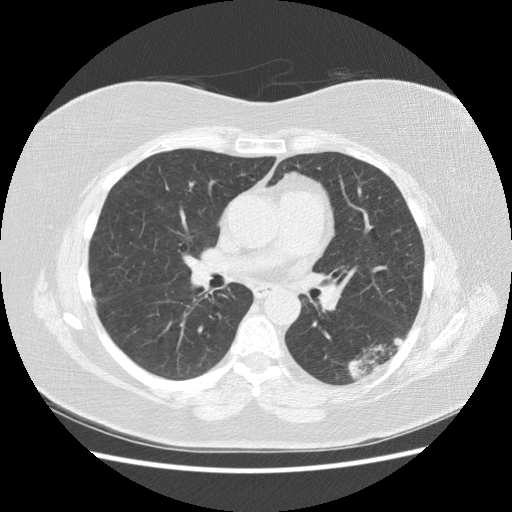
Low-dose screening chest CT, one axial slice. Slice 84 of 151 in the series (ordered by position). Reconstruction kernel STANDARD. Lung window (W 1500 / L -600 HU). 2.5 mm slice thickness. 512 × 512 image matrix, field of view 360 × 360 mm.
Annotated regions visible in this slice (manually delineated by an expert):
- lesion 1 (tumor, lower lobe of left lung): bounding box (x1, y1, x2, y2) in pixels: (348, 337, 404, 381)